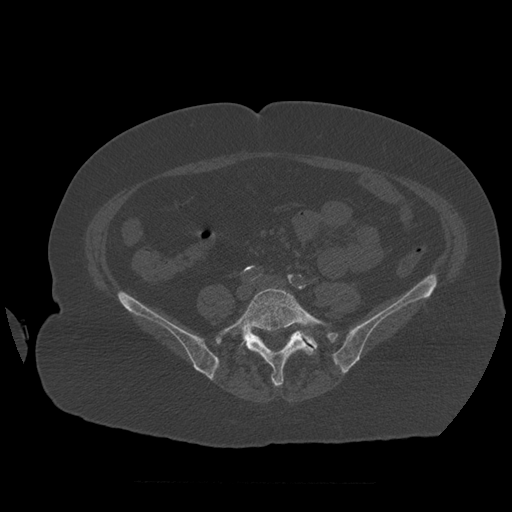
CT including the spine, one axial slice; slice 182 of 399 in the series (ordered by position); 120 kVp; bone window (W 1800 / L 400 HU); 1.25 mm slice thickness; 512 × 512 image matrix, field of view 404 × 404 mm. Patient age 81 years. From the clinical record (not read from this slice): primary cancer: renal.
Outlined on this slice (semi-automatically segmented with operator editing):
- L5 vertebra: bounding box (x1, y1, x2, y2) in pixels: (219, 288, 329, 387)